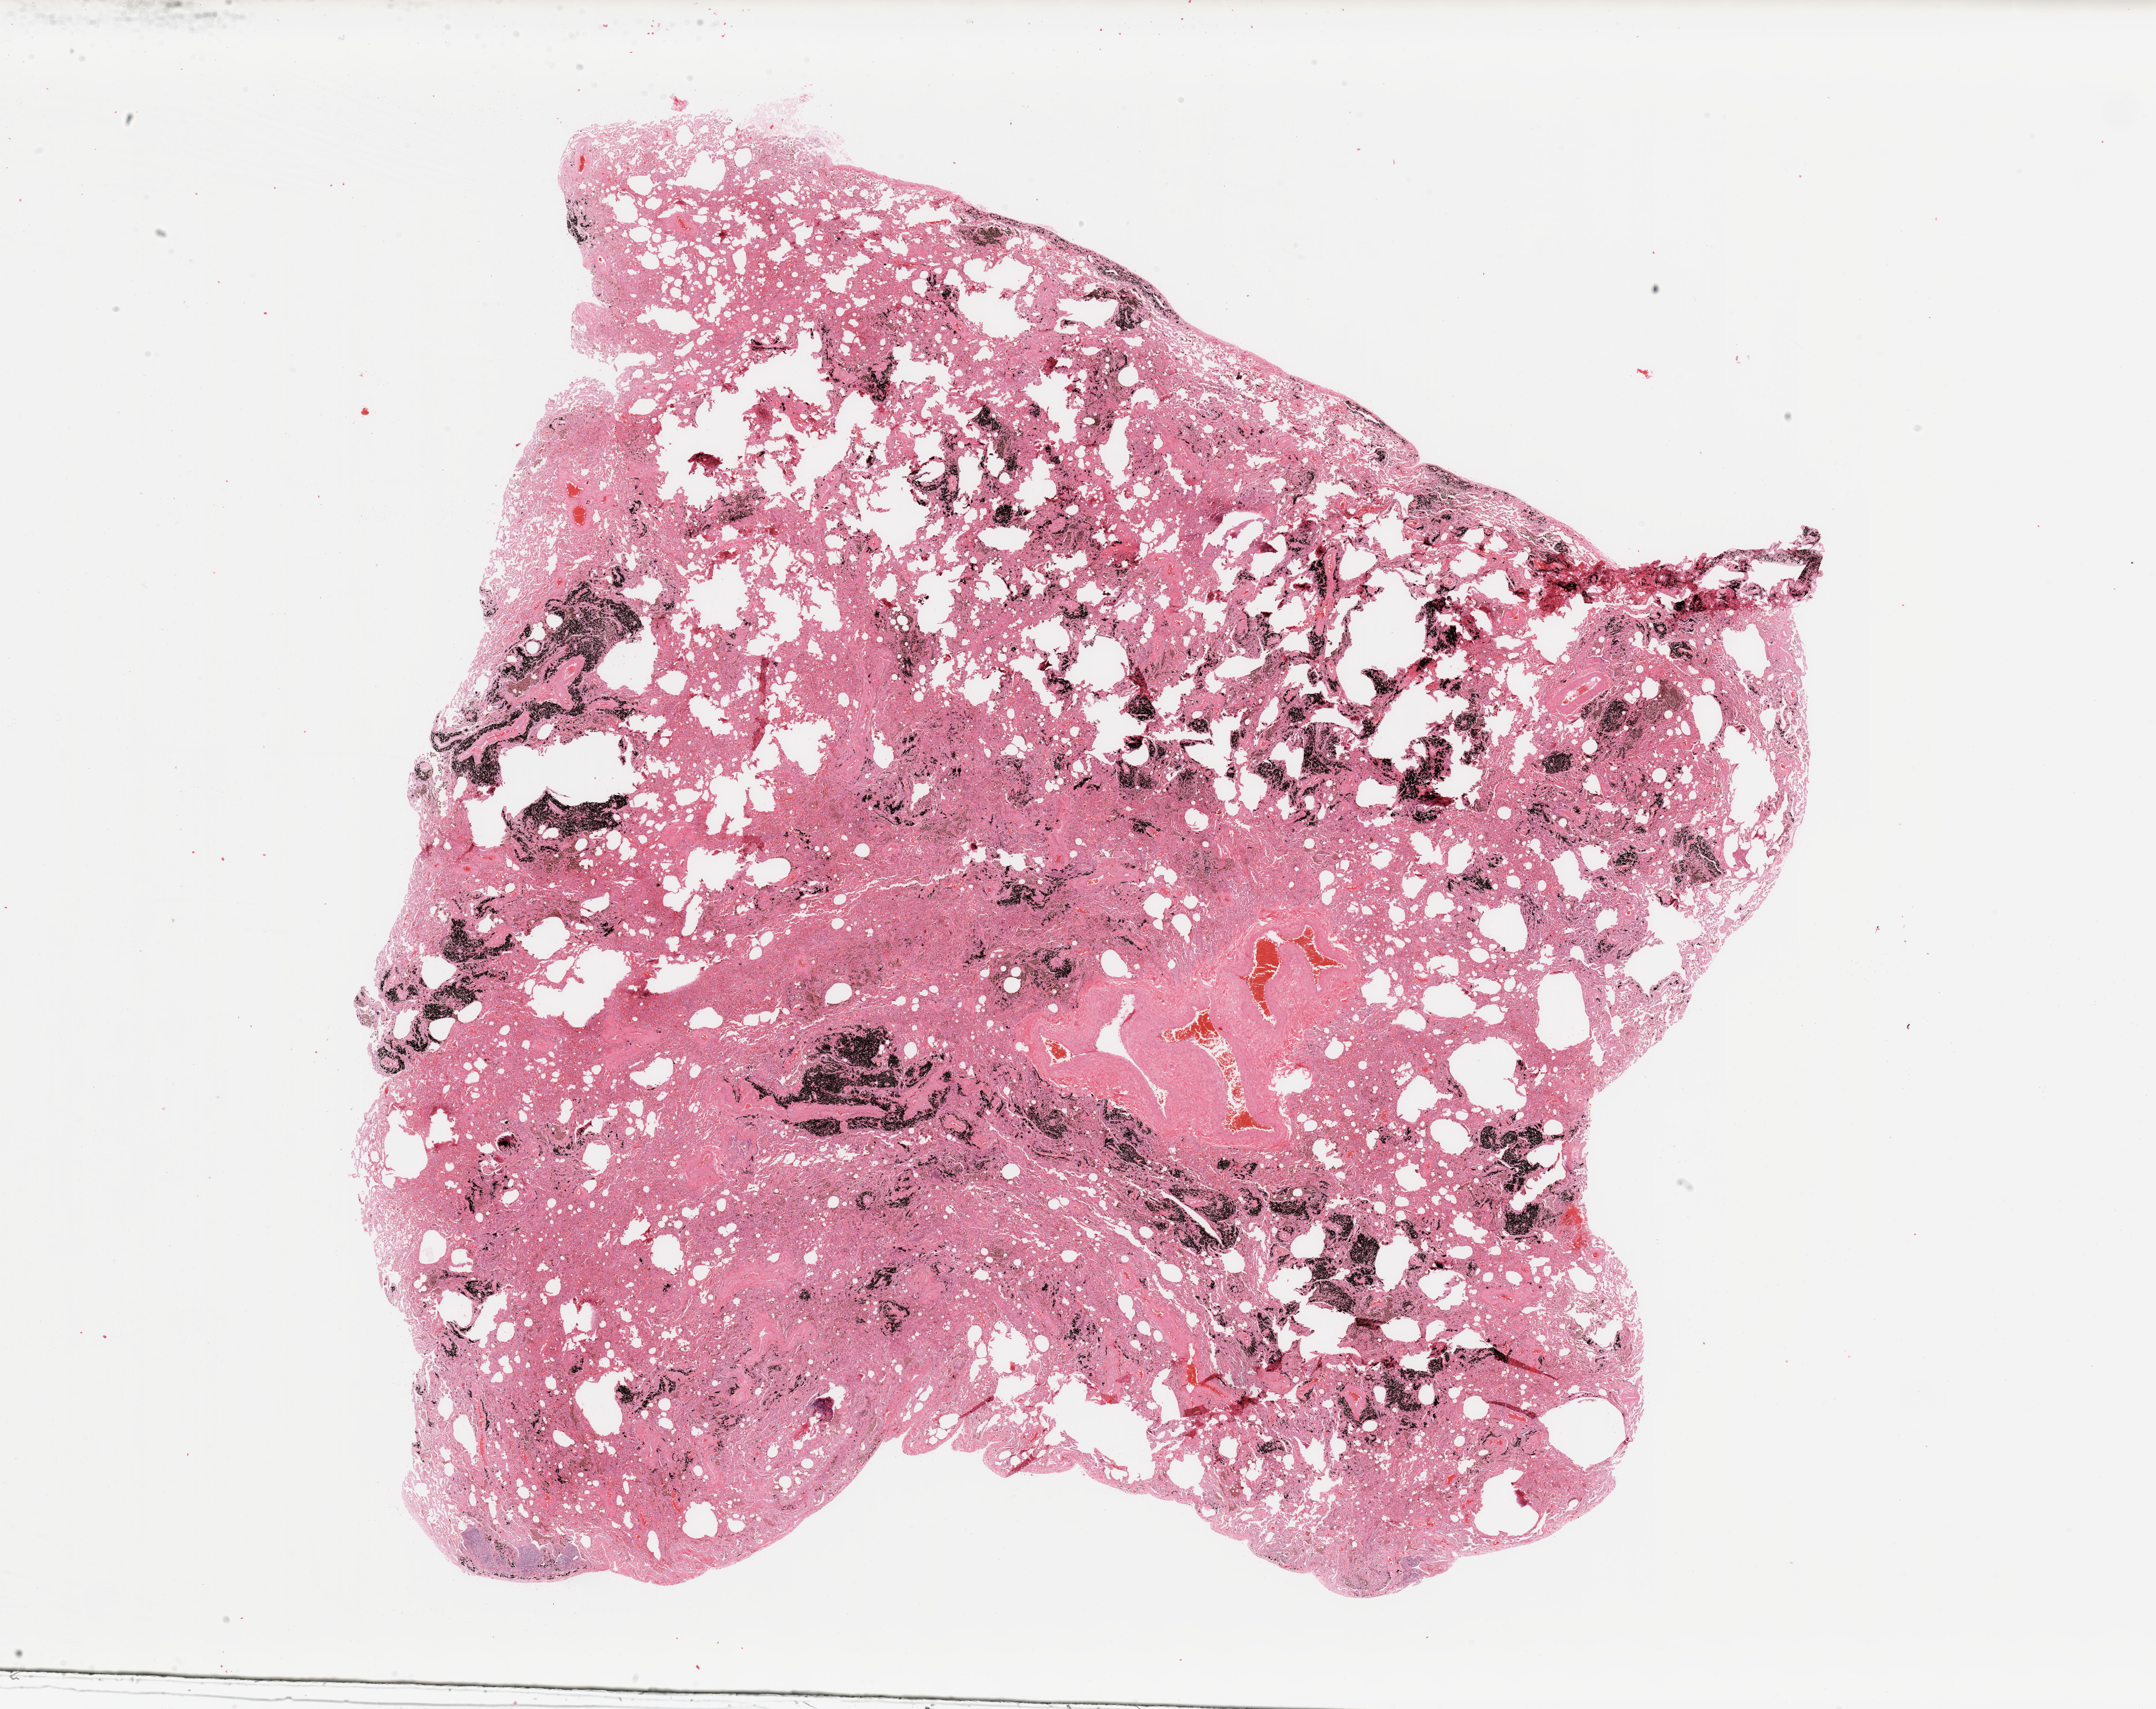
H&E-stained whole-slide image — low-resolution overview of the scanned area, about 29.5 x 23.4 mm (acquisition: 20x scan); normal (non-tumour) tissue sample, sampled site: lung. 56-year-old male patient.
This section: normal (non-tumour) tissue from the same patient. Patient diagnosis: Adenocarcinoma, NOS.